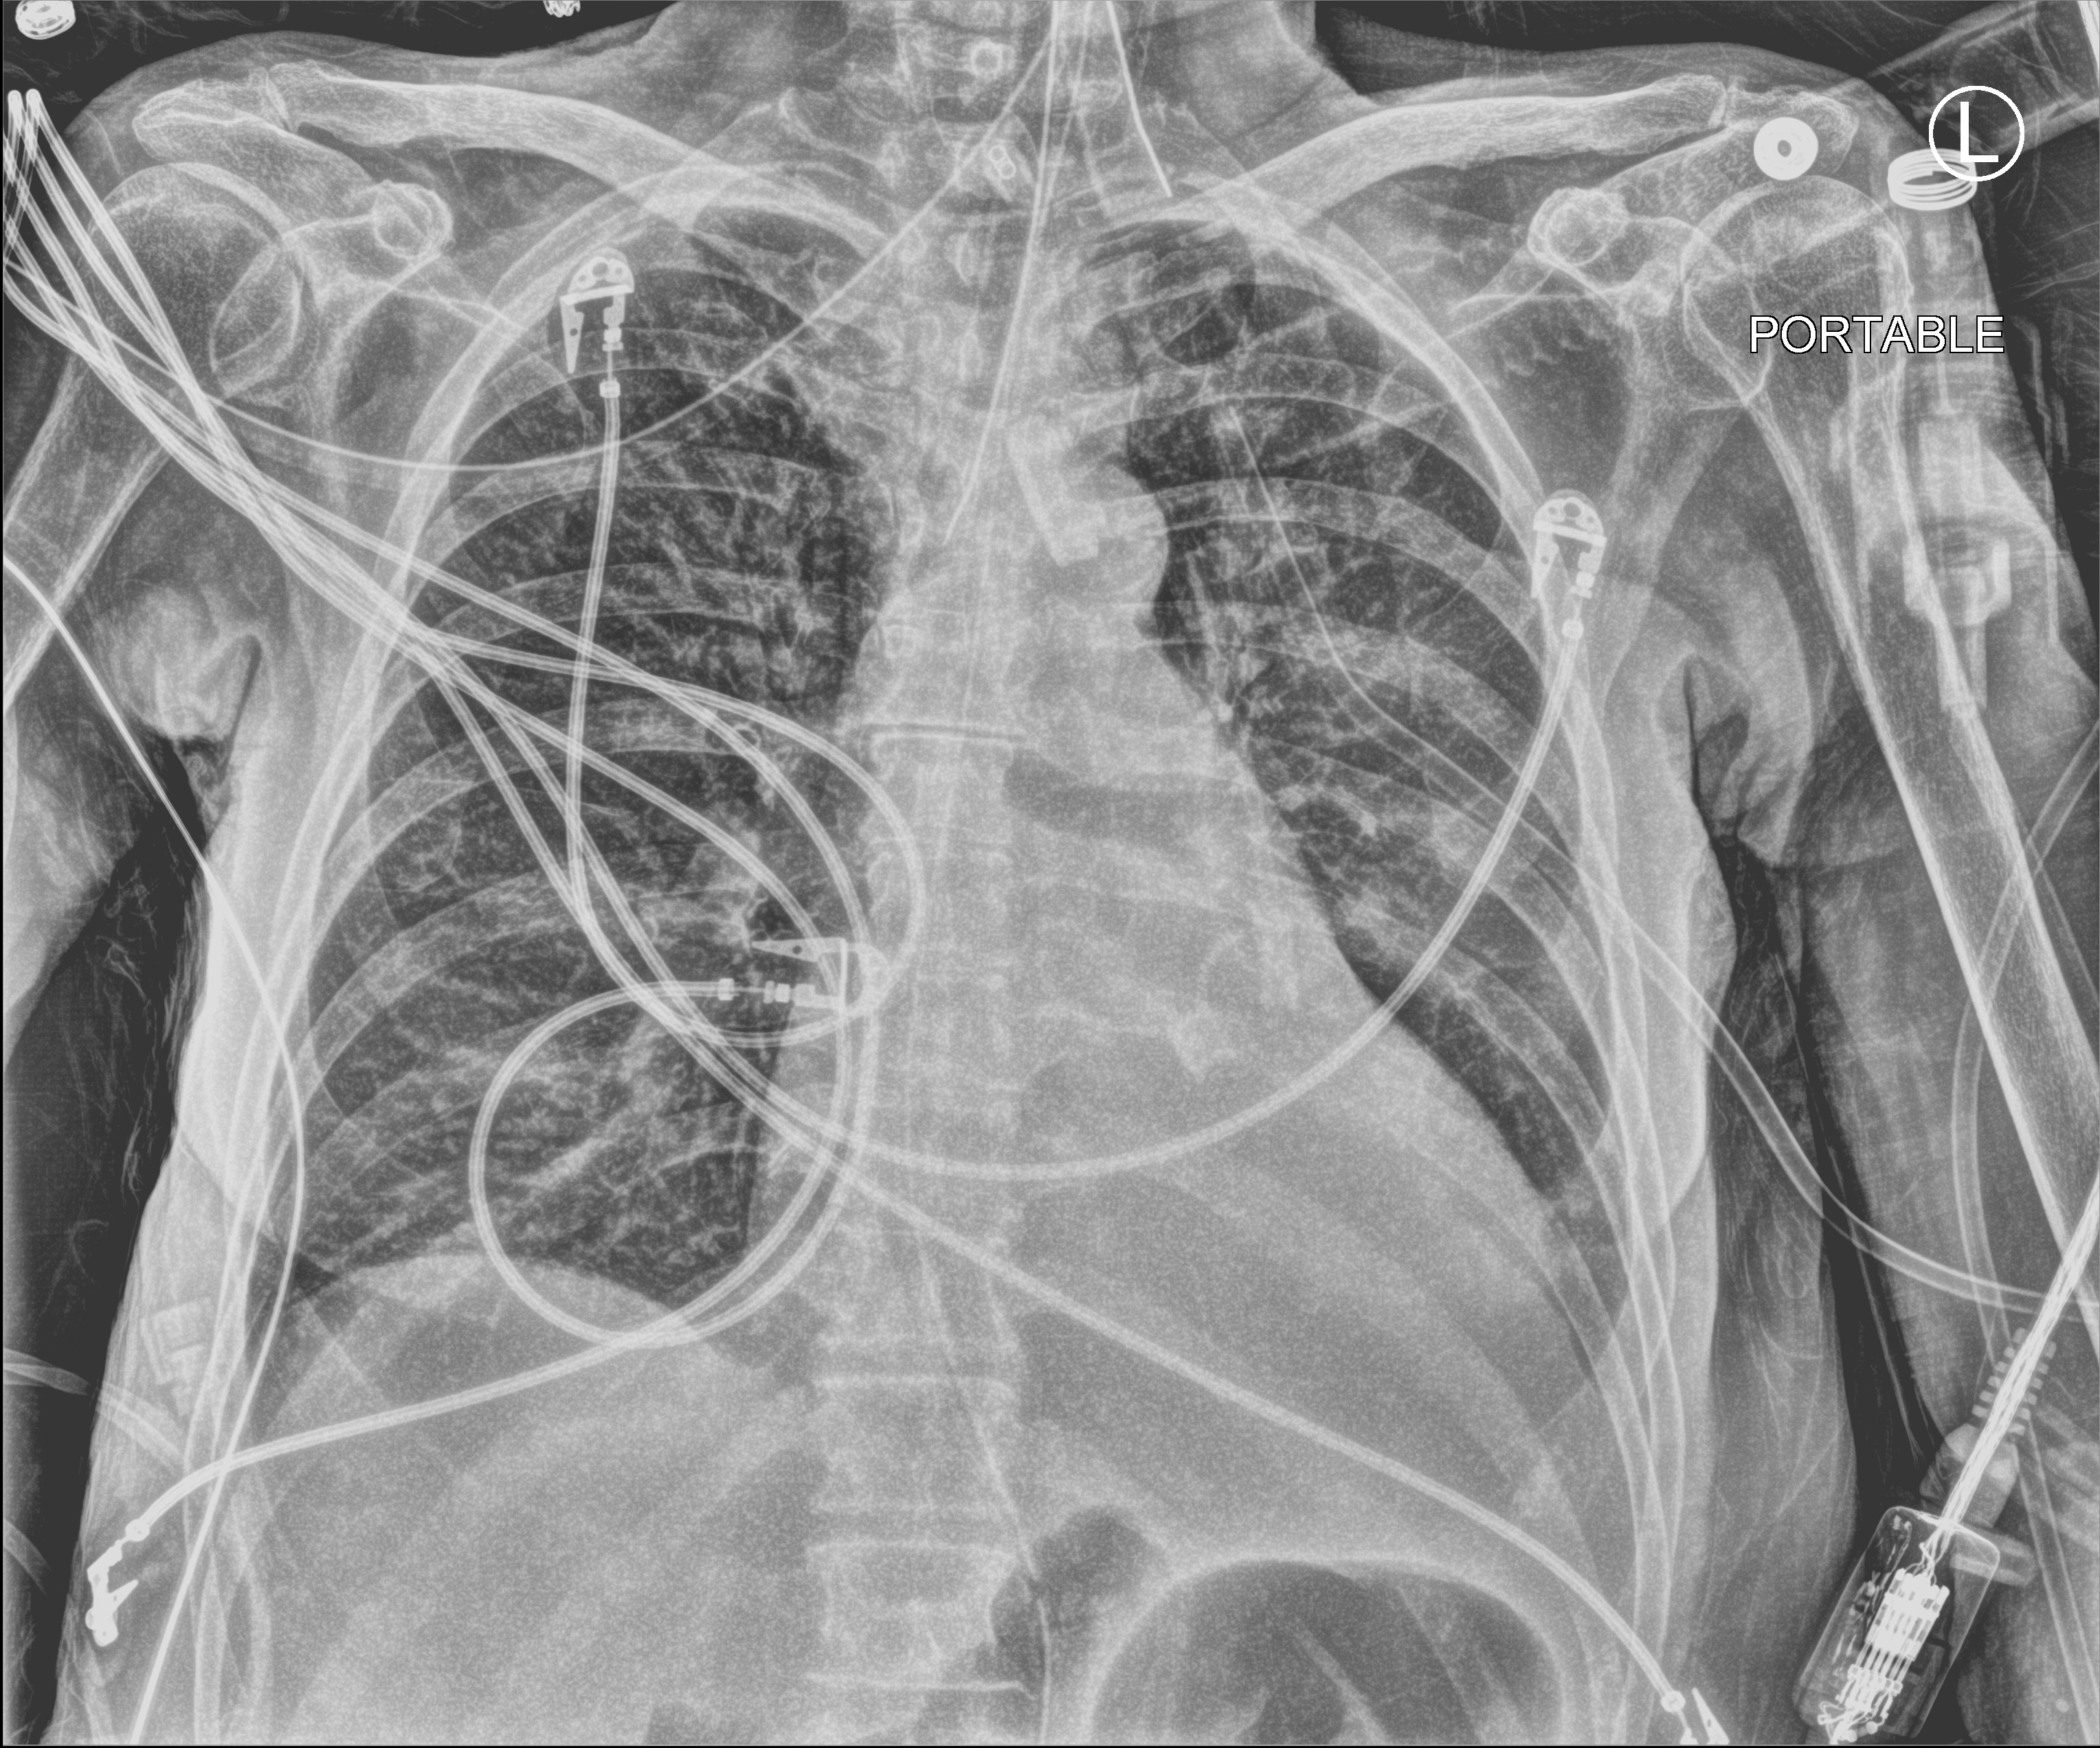
Portable chest radiograph, anteroposterior (AP) projection. Patient hospitalised with COVID-19; female, aged 60–74 years.
Hospital-stay facts (about this admission, not read from this image; timing relative to this image not recorded):
- length of hospital stay: 38 days
- admitted to intensive care during this hospital stay: yes